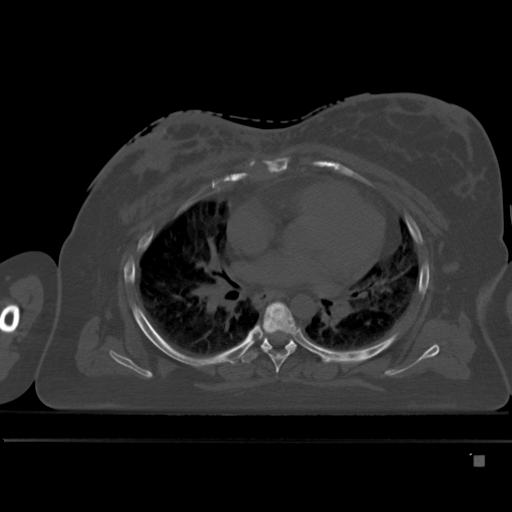
CT including the spine, one axial slice. Position 313 of 495 along the scan axis. Bone window (W 1800 / L 400 HU). 512 × 512 image matrix. Female patient, age 33 years. From the clinical record (not read from this slice): primary cancer: breast; vertebrae with lytic lesions (as recorded): T1.
Annotated regions visible in this slice (semi-automatically segmented with operator editing):
- T5 vertebra: bounding box [x1, y1, x2, y2] px = [263, 302, 297, 373]
- T6 vertebra: [242, 334, 299, 364]